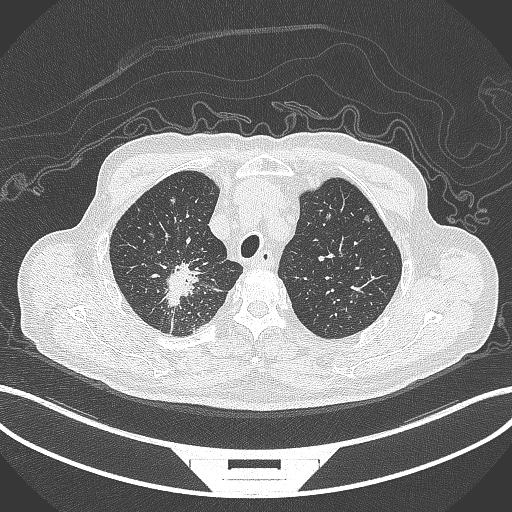
Chest CT, one axial slice; position 307 of 407 along the scan axis; reconstruction kernel B70f; 120 kVp; lung window (W 1500 / L -600 HU); 1 mm slice thickness; 512 × 512 image matrix. Male patient, age 69 years. From the clinical record (not read from this slice): clinical TNM (as recorded): T1c N1 M1.
Annotated regions visible in this slice (bounding box drawn by a radiologist):
- lung tumour (recorded histology: adenocarcinoma): bounding box (x1, y1, x2, y2) in pixels: (163, 261, 209, 315)